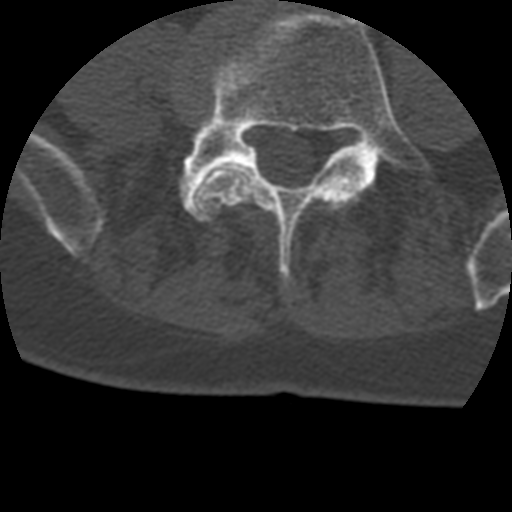
CT including the spine, one axial slice; position 49 of 399 along the scan axis; bone window (W 1800 / L 400 HU); 1.25 mm slice thickness; 512 × 512 image matrix, field of view 160 × 160 mm. Patient age 69 years. Case-level facts recorded for this patient, not image findings: primary cancer: prostate.
Outlined on this slice (semi-automatic segmentation, software-assisted and operator-edited):
- L4 vertebra: bounding box (x1, y1, x2, y2) in pixels: (174, 59, 360, 217)
- L5 vertebra: (179, 9, 430, 279)